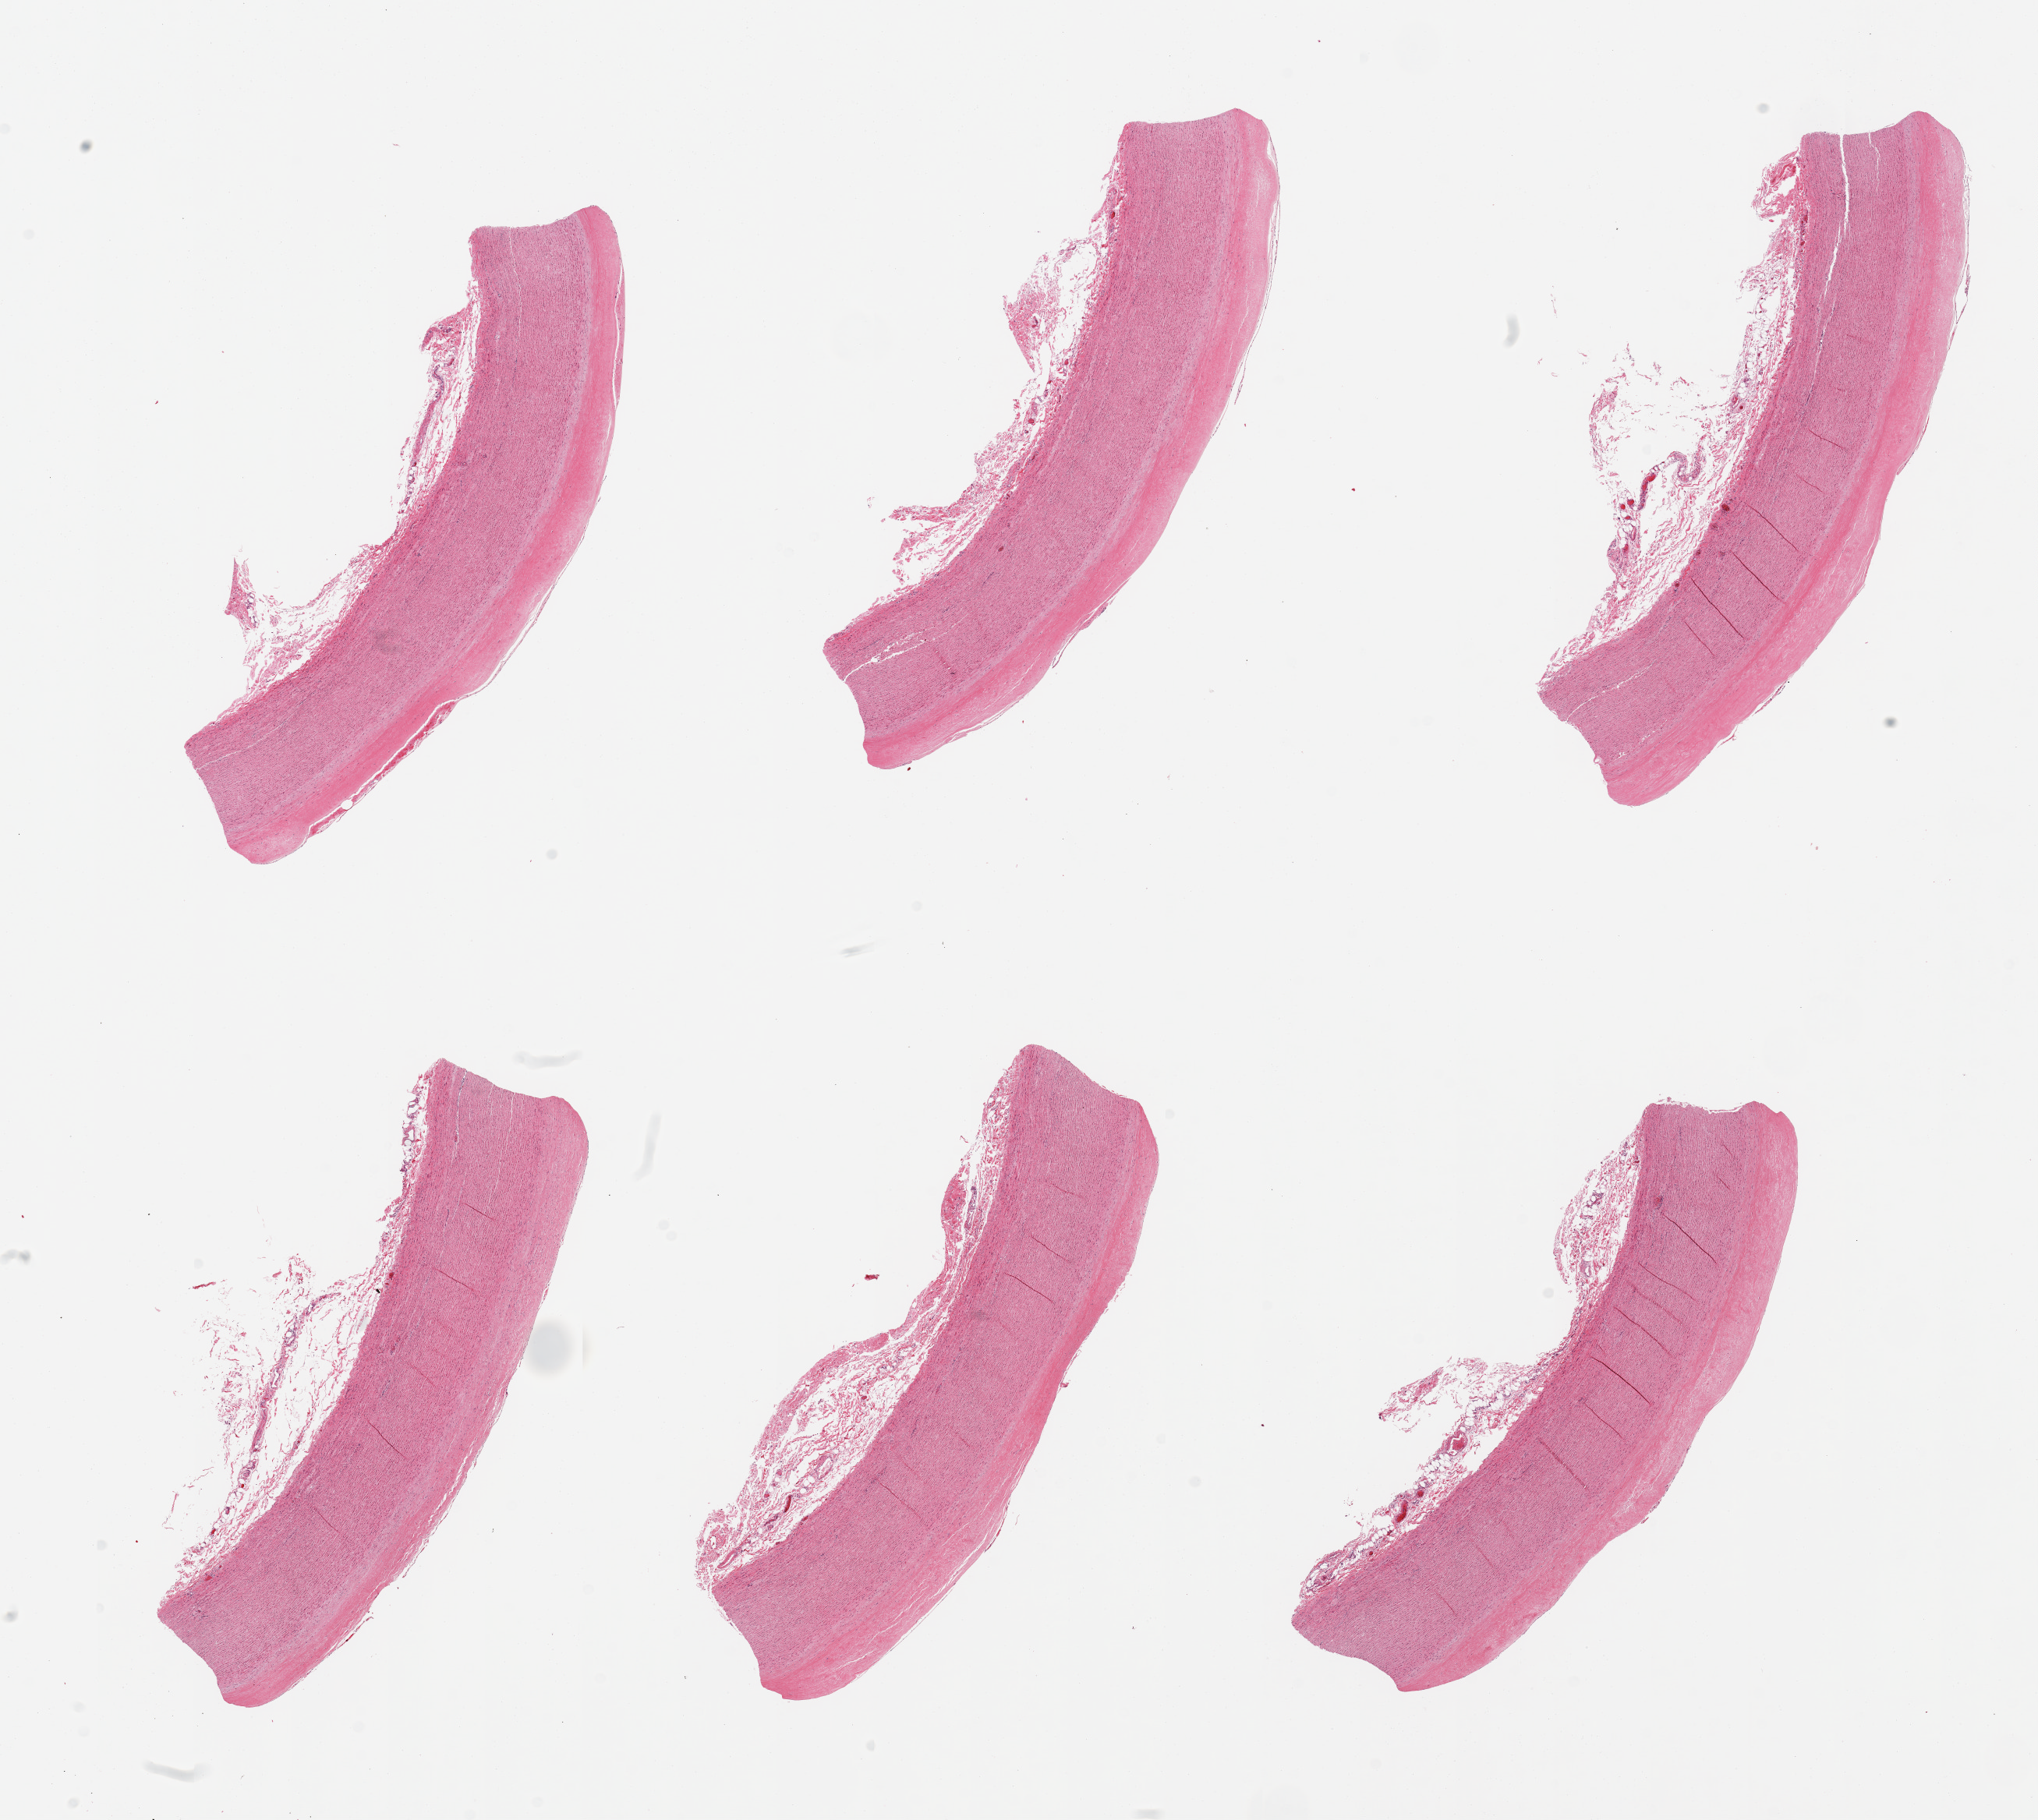
Whole-slide image, hematoxylin and eosin (H&E) stain, brightfield — low-resolution overview of the scanned area, about 20.7 x 18.5 mm. PAXgene-fixed, paraffin-embedded tissue. Target tissue: aorta. Tissue donor sample. Donor sex: male.
* pathologist's review note for this sample: 6 pieces, diffuse atherosis up to ~0.5mm; adherent serosa up to ~0.8mm